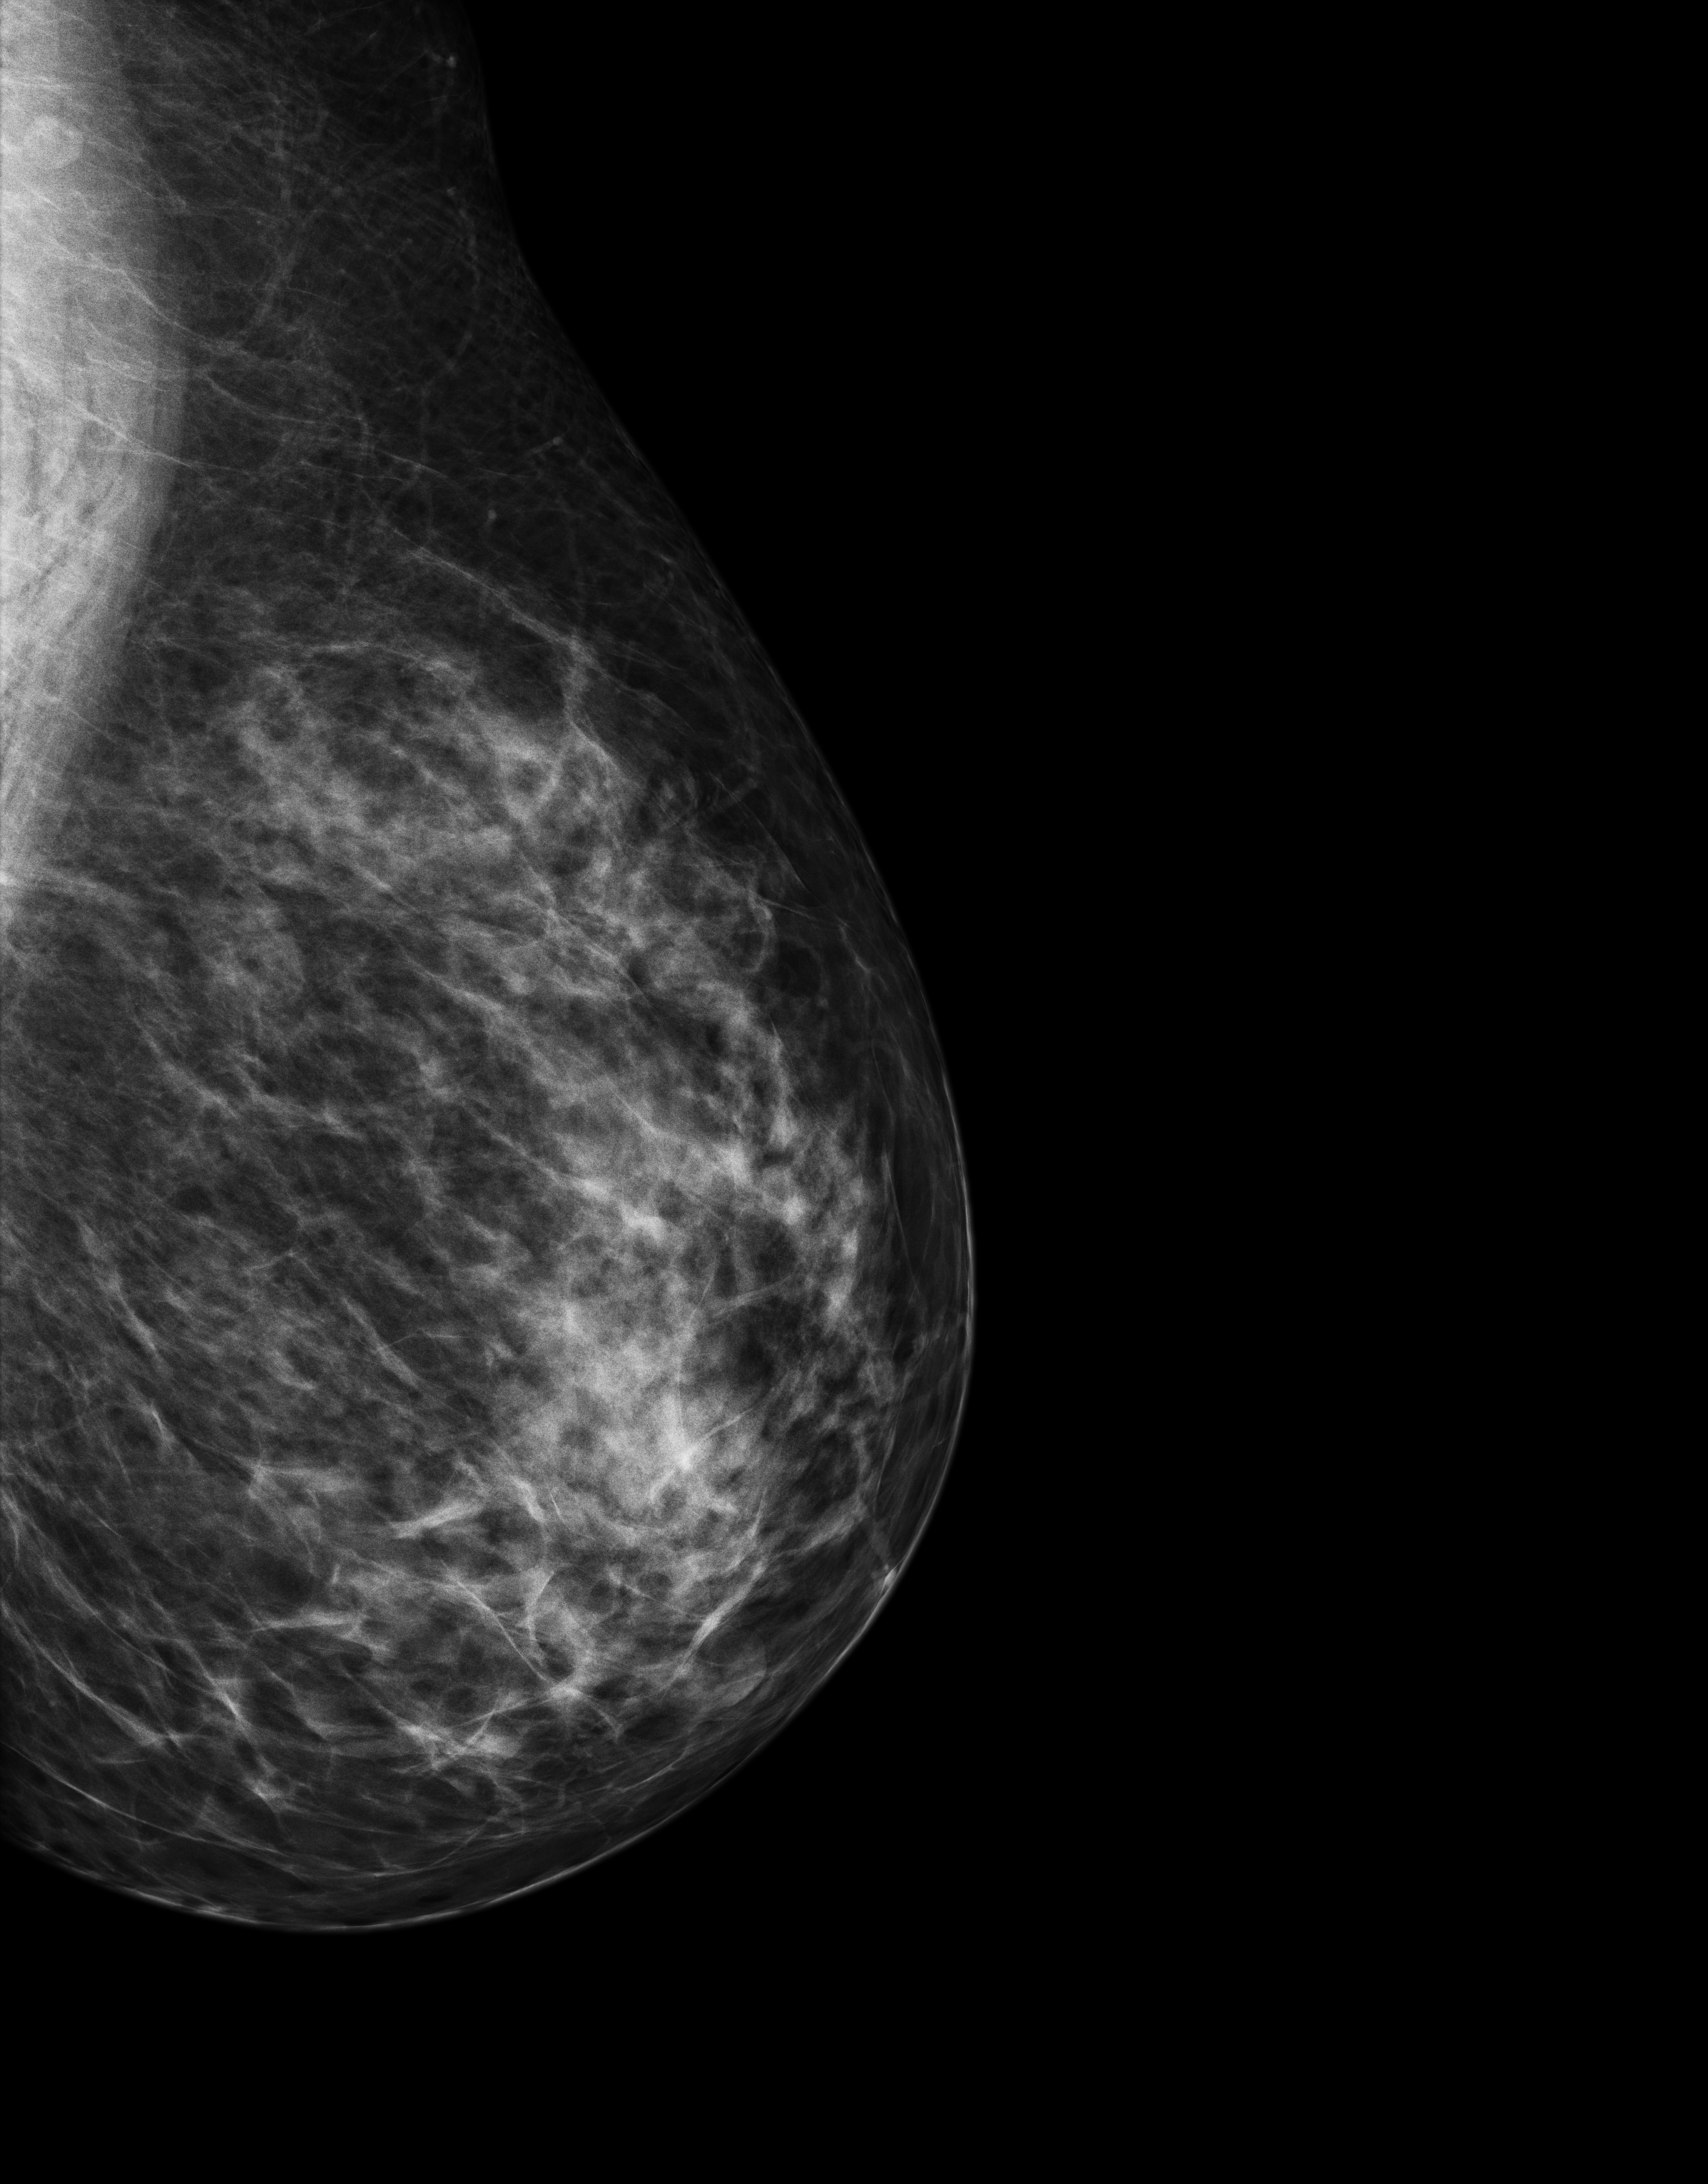
Screening examination. Patient: female, 43 years.
Image type: full-field digital mammogram. Breast: left. Projection: exaggerated CC view (lateral).